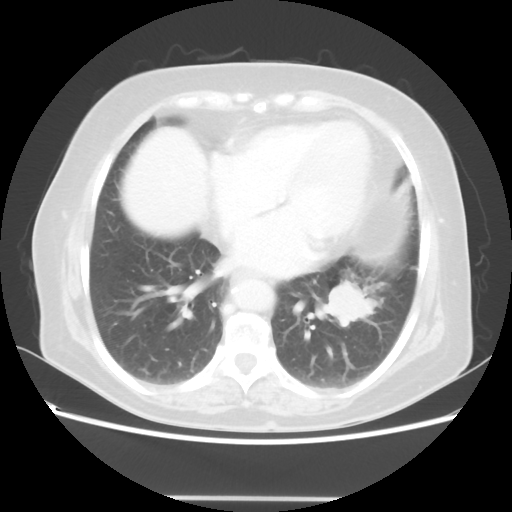
Chest CT, one axial slice; position 22 of 56 along the scan axis; reconstruction kernel STANDARD; 100 kVp; lung window (W 1500 / L -600 HU); 5 mm slice thickness; 512 × 512 image matrix. Patient: female, 73 years. From the clinical record (not read from this slice): clinical TNM (as recorded): T1c N0 M0.
Outlined on this slice (rectangle marked by the reading radiologist):
- lung tumour (recorded histology: adenocarcinoma): bounding box [x1, y1, x2, y2] px = [317, 277, 381, 330]